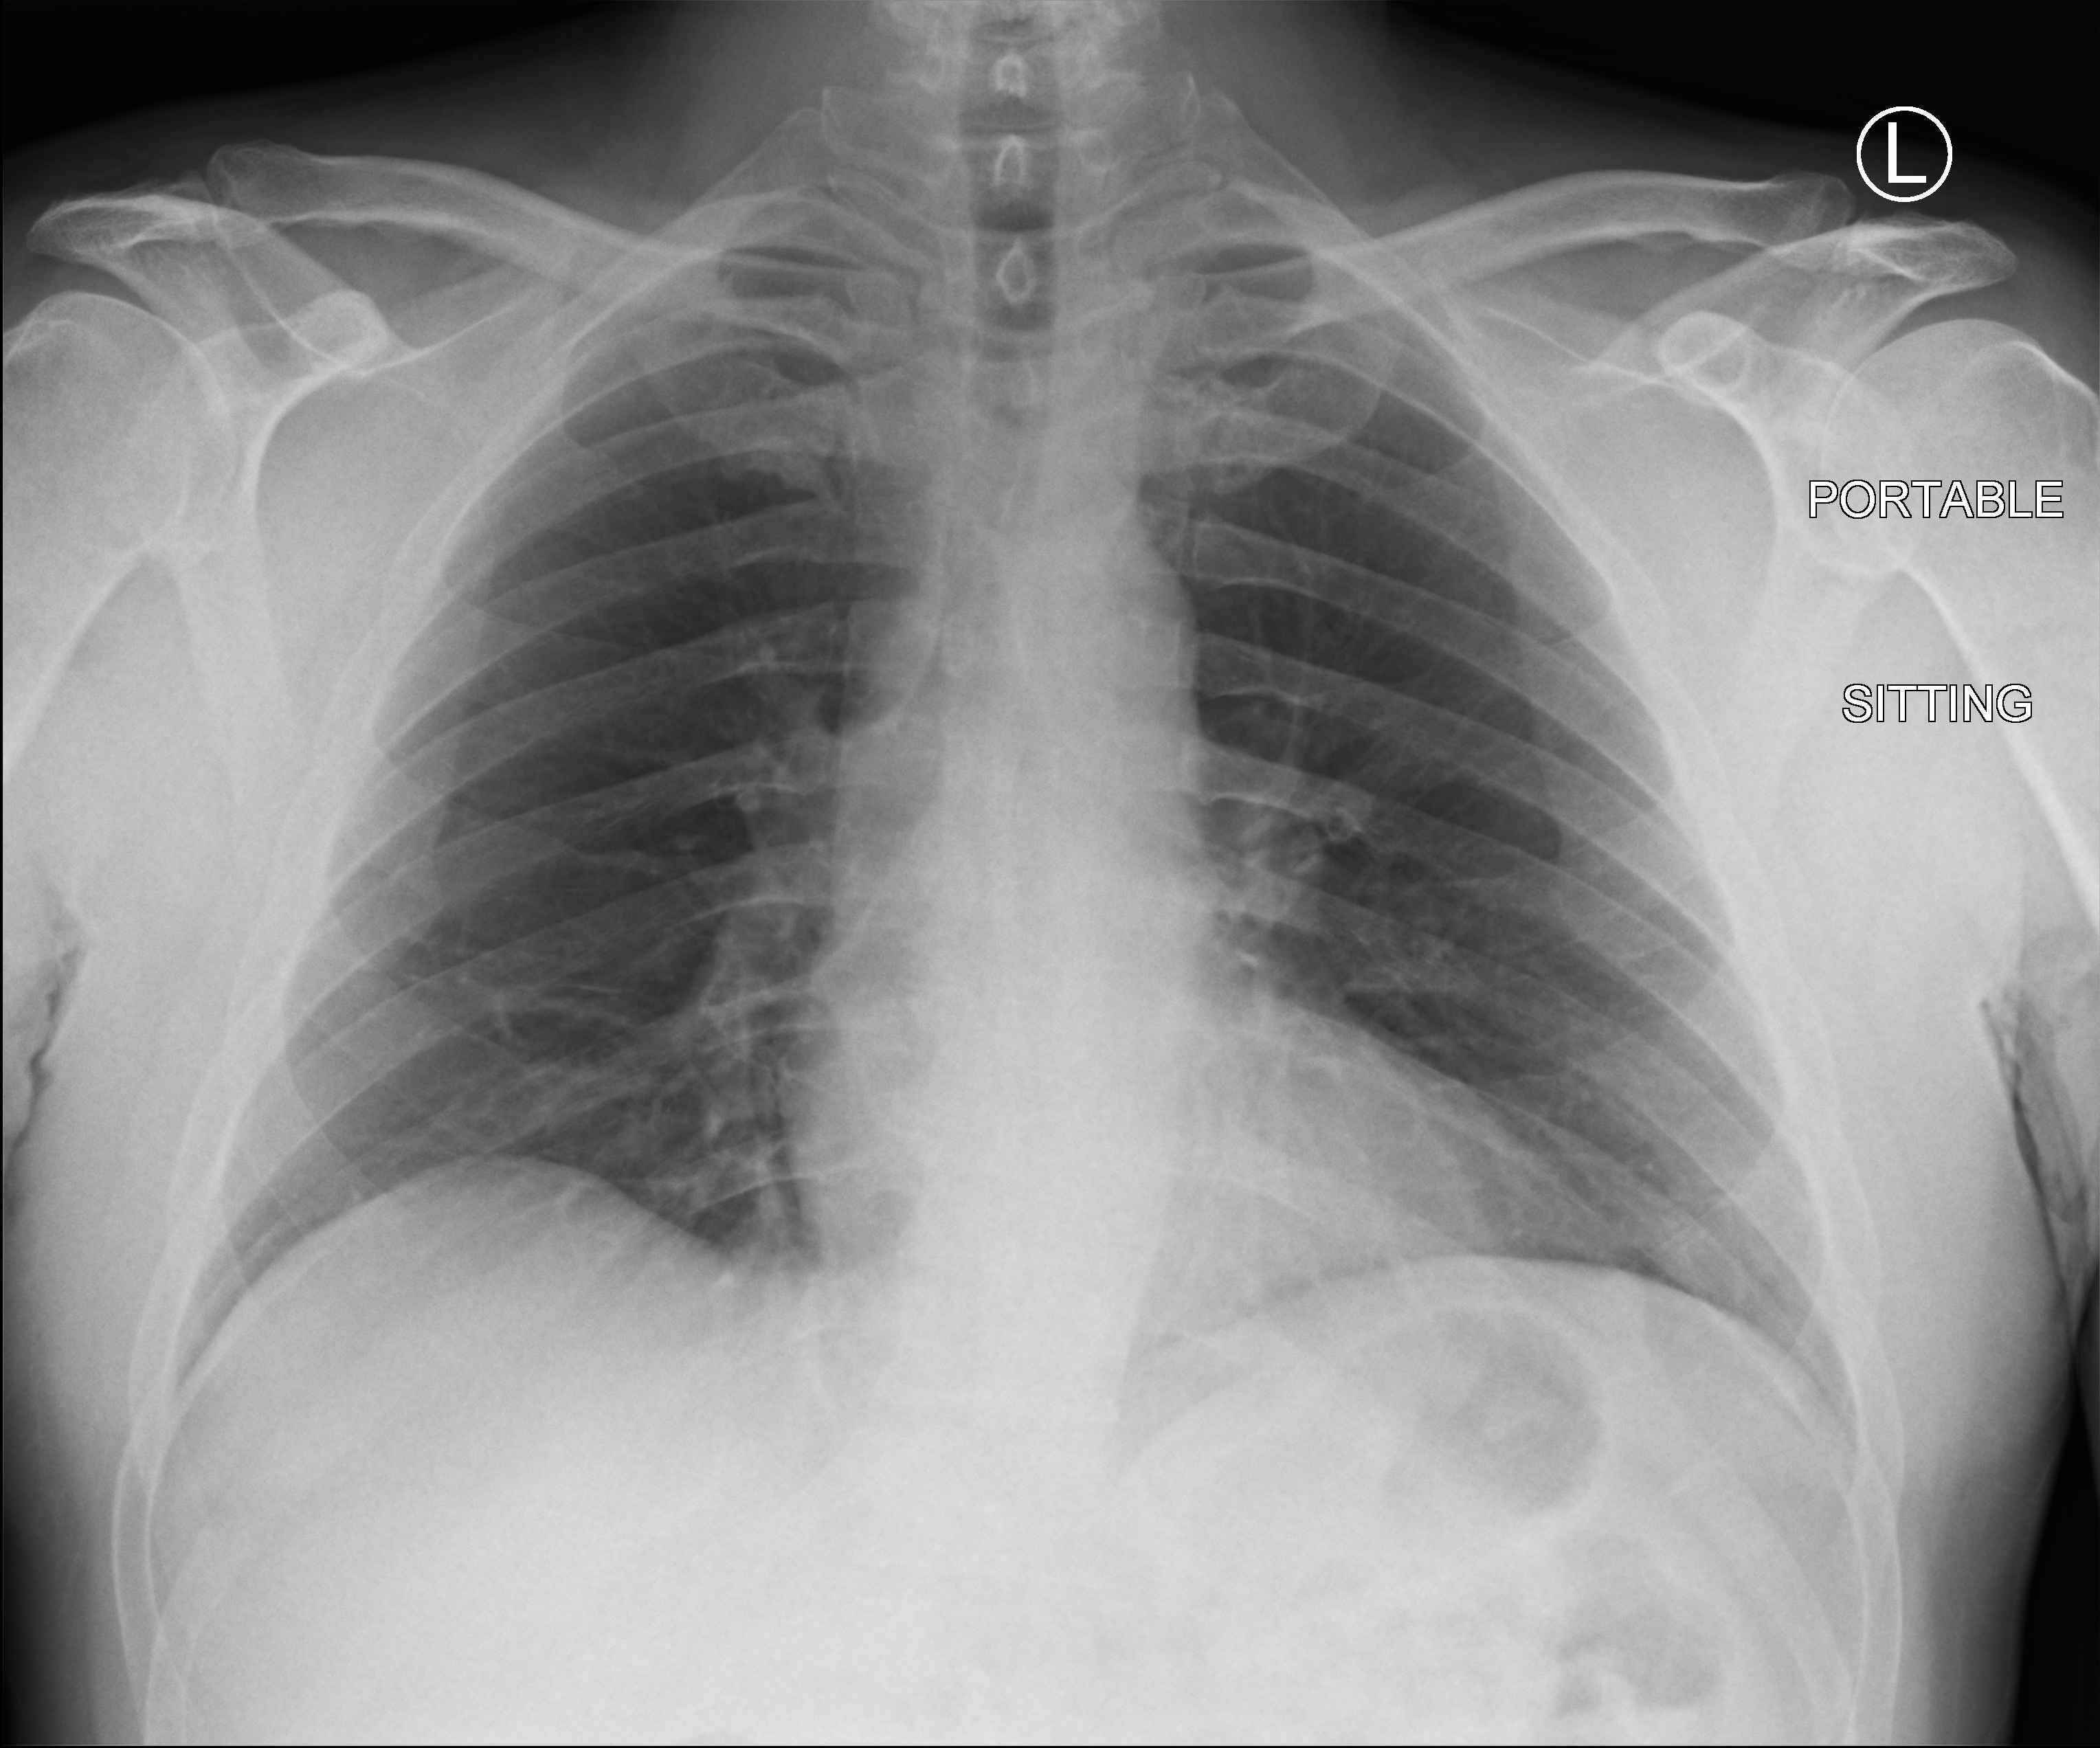
Bedside chest radiograph (computed radiography). Male patient hospitalised with COVID-19, age 18–59 years.
Admission-level facts for this patient (not findings on this image; timing relative to this image not recorded): mechanically ventilated during this hospital stay: no.